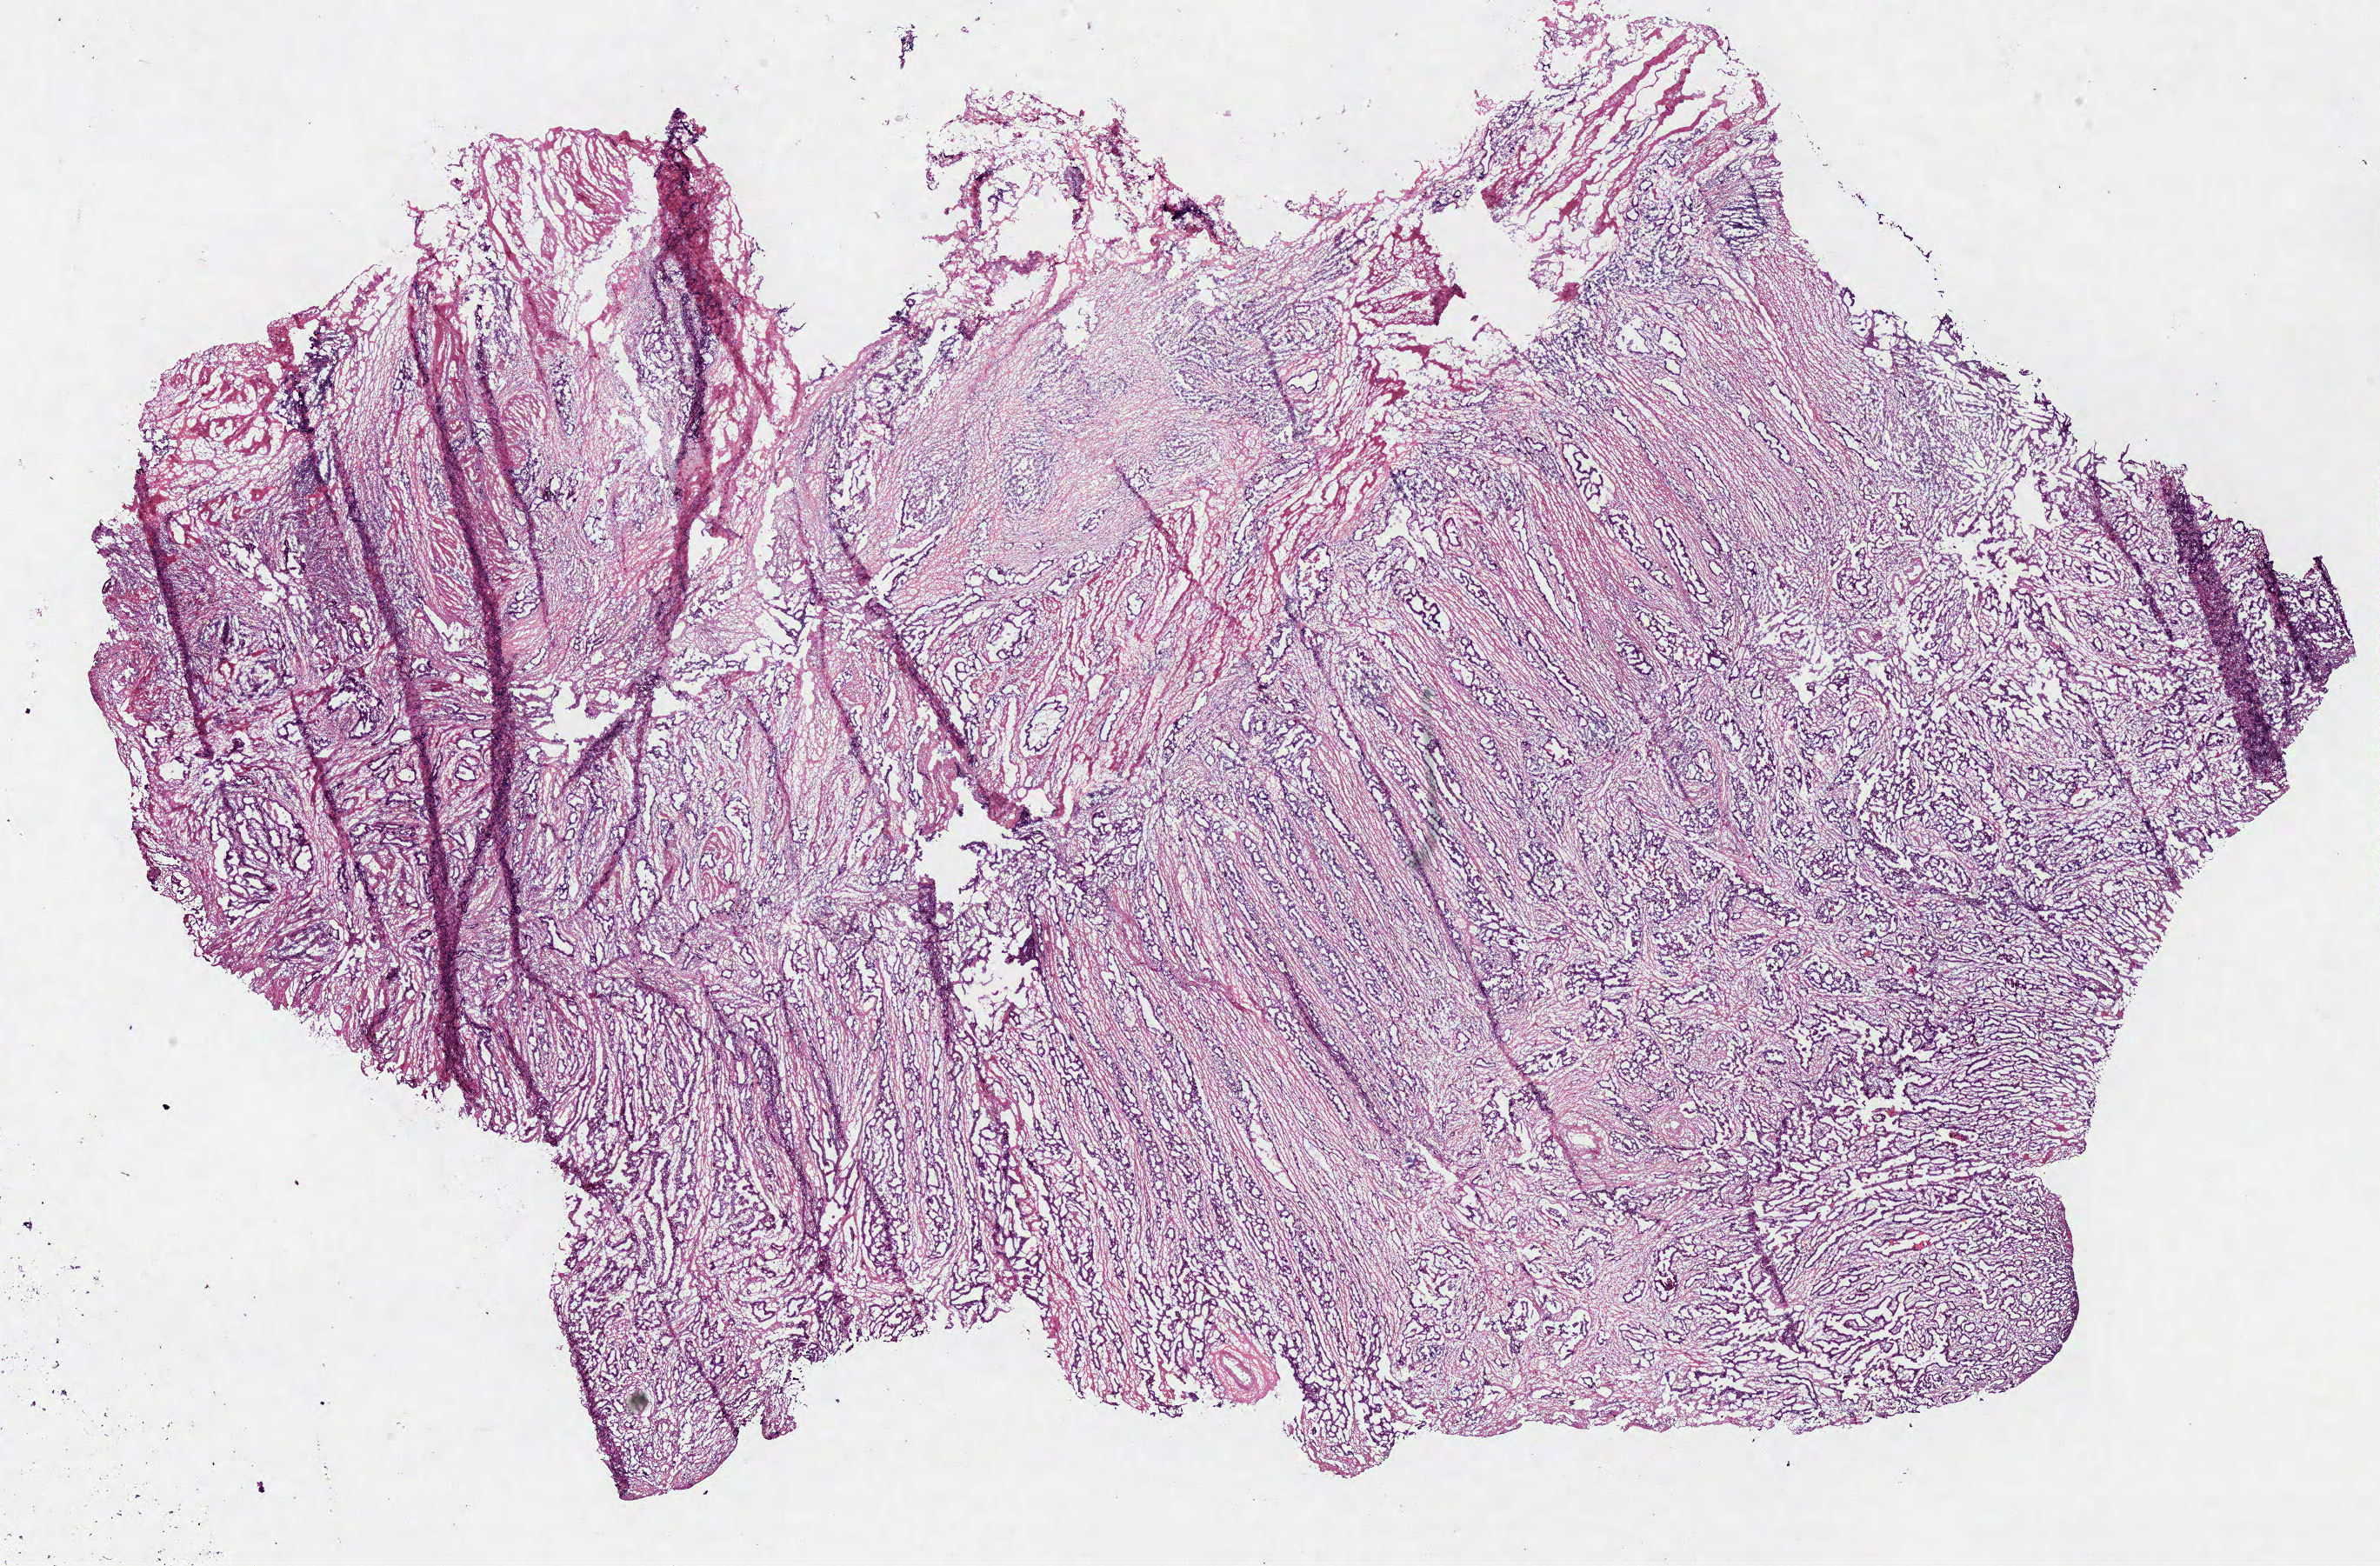
Digitized H&E tissue section (whole slide), a low-resolution overview of the entire scanned area, about 21.6 x 14.2 mm, frozen section from the top of the tissue portion, primary tumour sample from the rectum. Male, age 67 years at initial diagnosis. Composition of this section per pathologist review: tumour cells 95%, tumour nuclei 70%, stromal cells 4%, necrosis 1%. Inflammatory infiltration, as recorded: lymphocyte infiltration 10%.
Pathologic diagnosis: Adenocarcinoma, NOS (connective, subcutaneous and other soft tissues of abdomen). AJCC pathologic stage: IIA (7th edition).